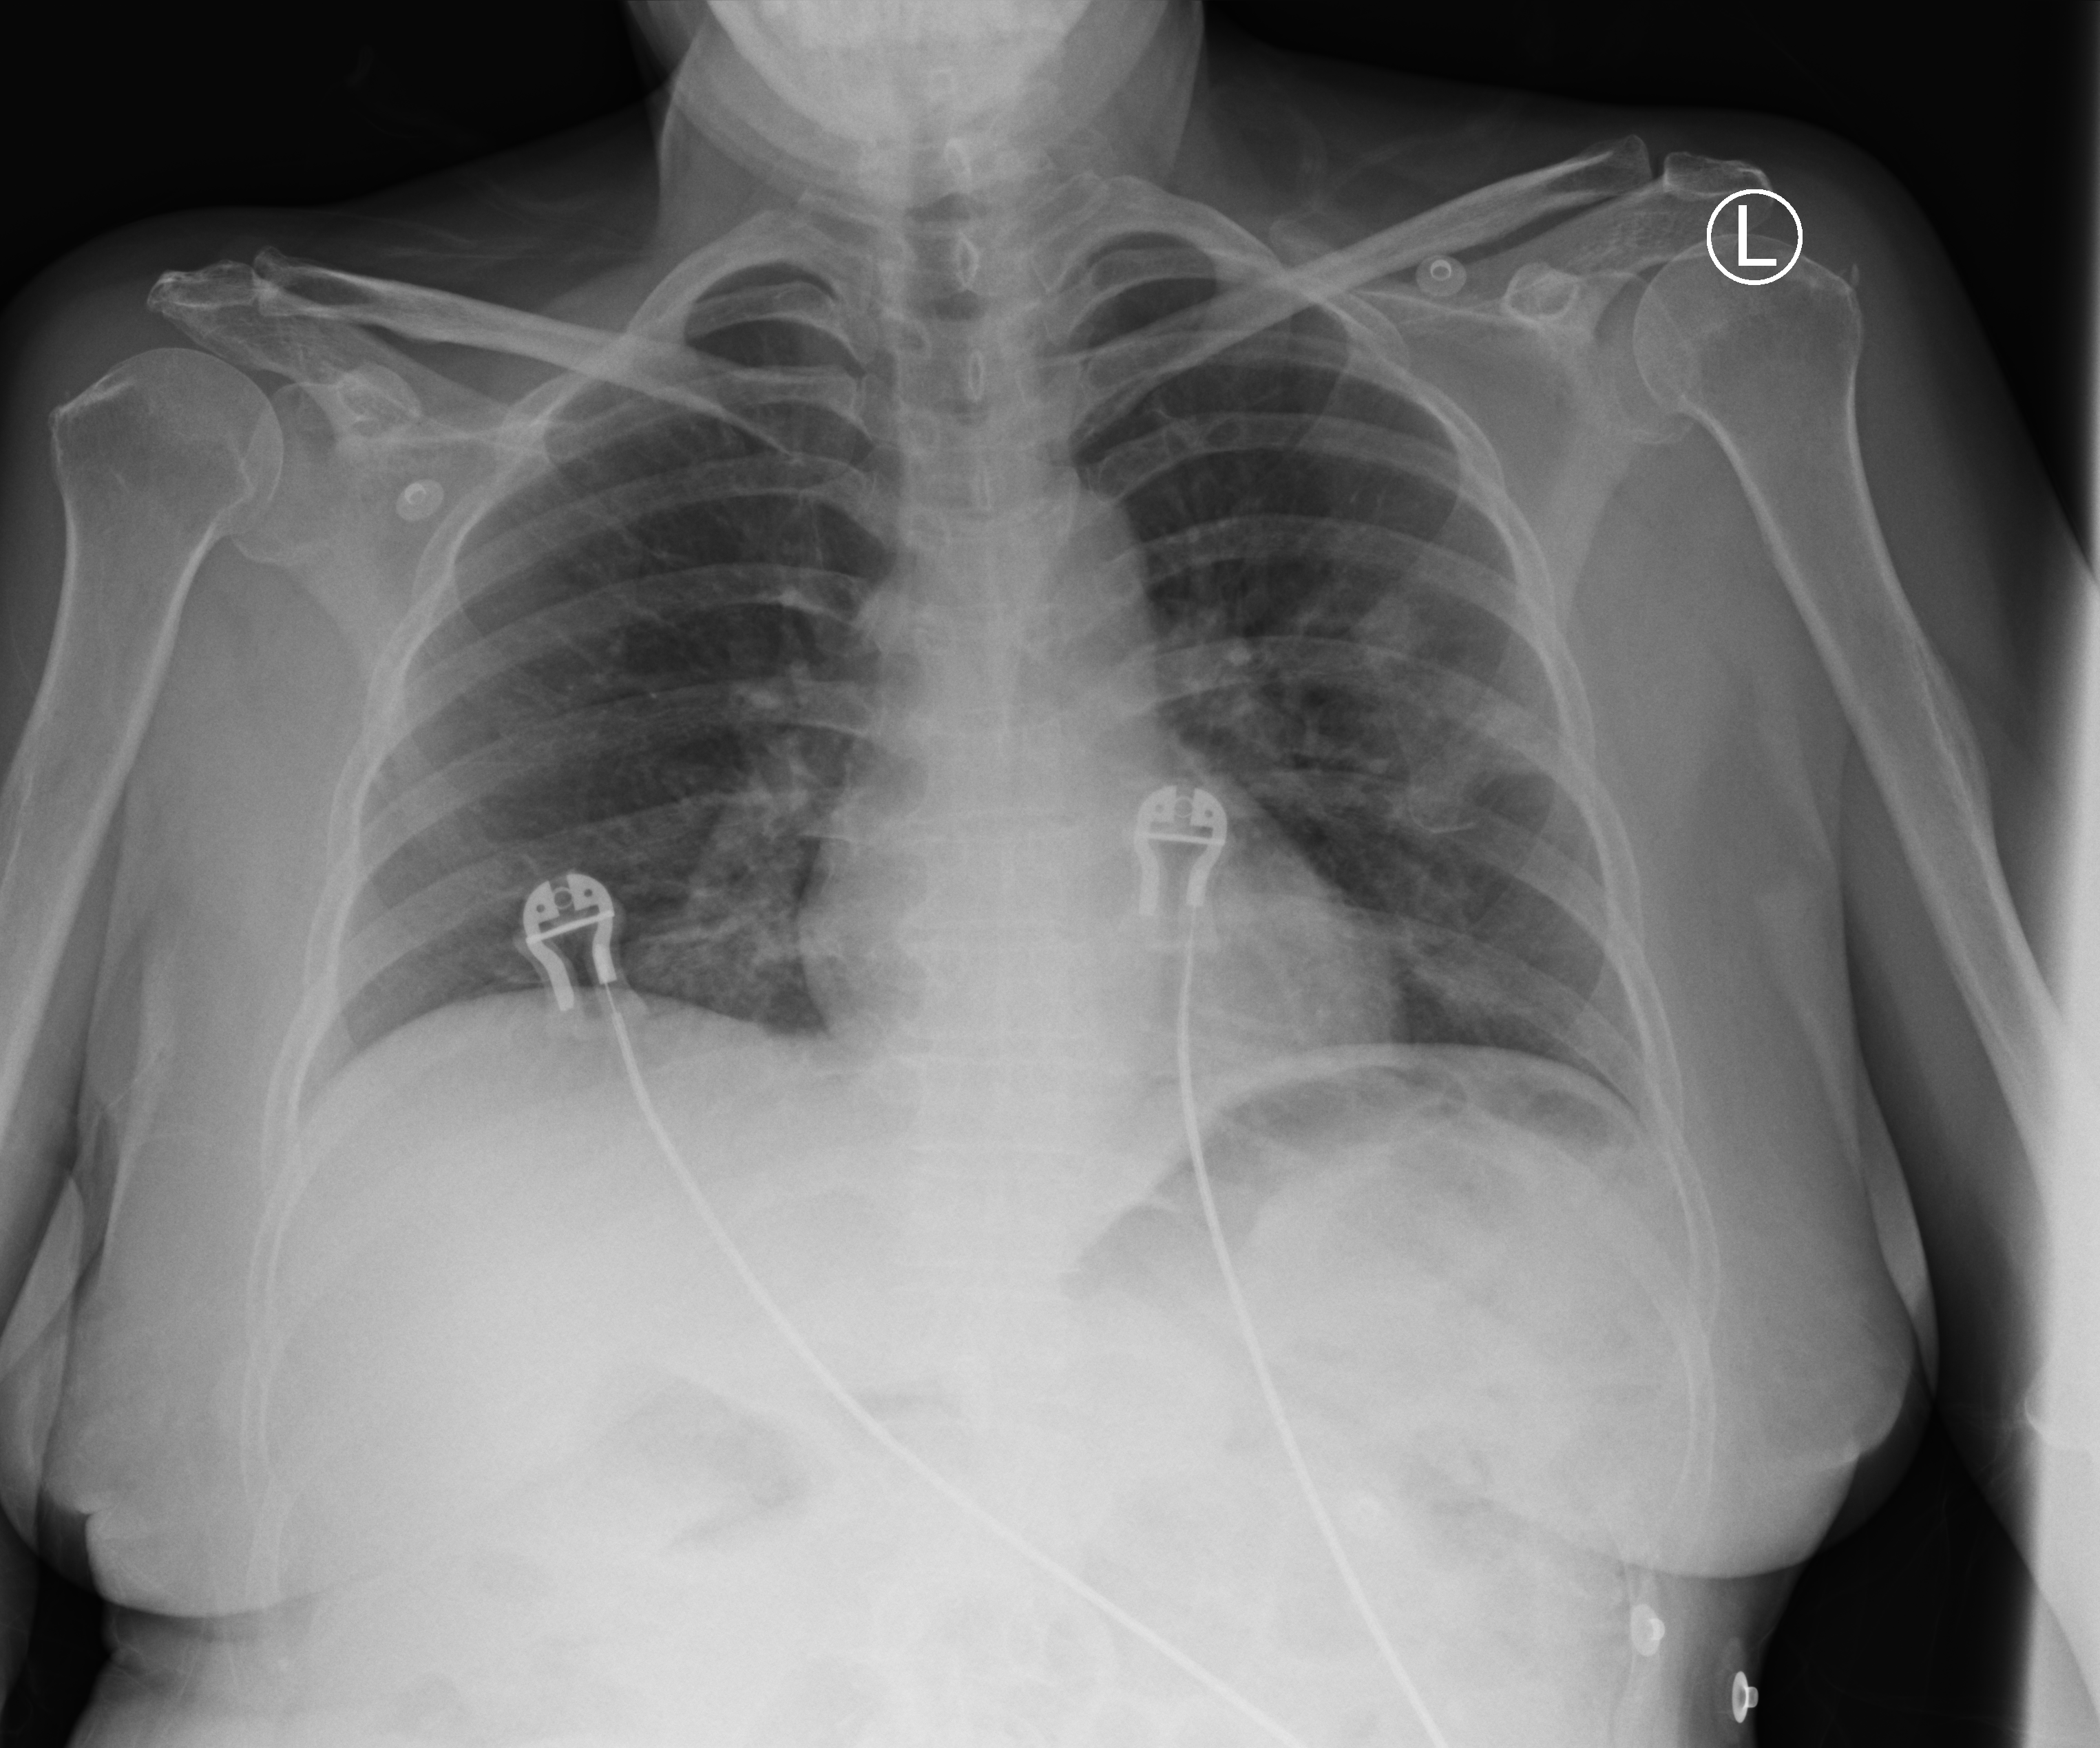
Chest X-ray (portable); anteroposterior (AP) projection. Female patient hospitalised with COVID-19, age 18–59 years.
From the hospital-stay record, not from the radiograph (when in the stay this image was taken is not recorded):
- COPD (admission record): no
- admitted to intensive care during this hospital stay: no